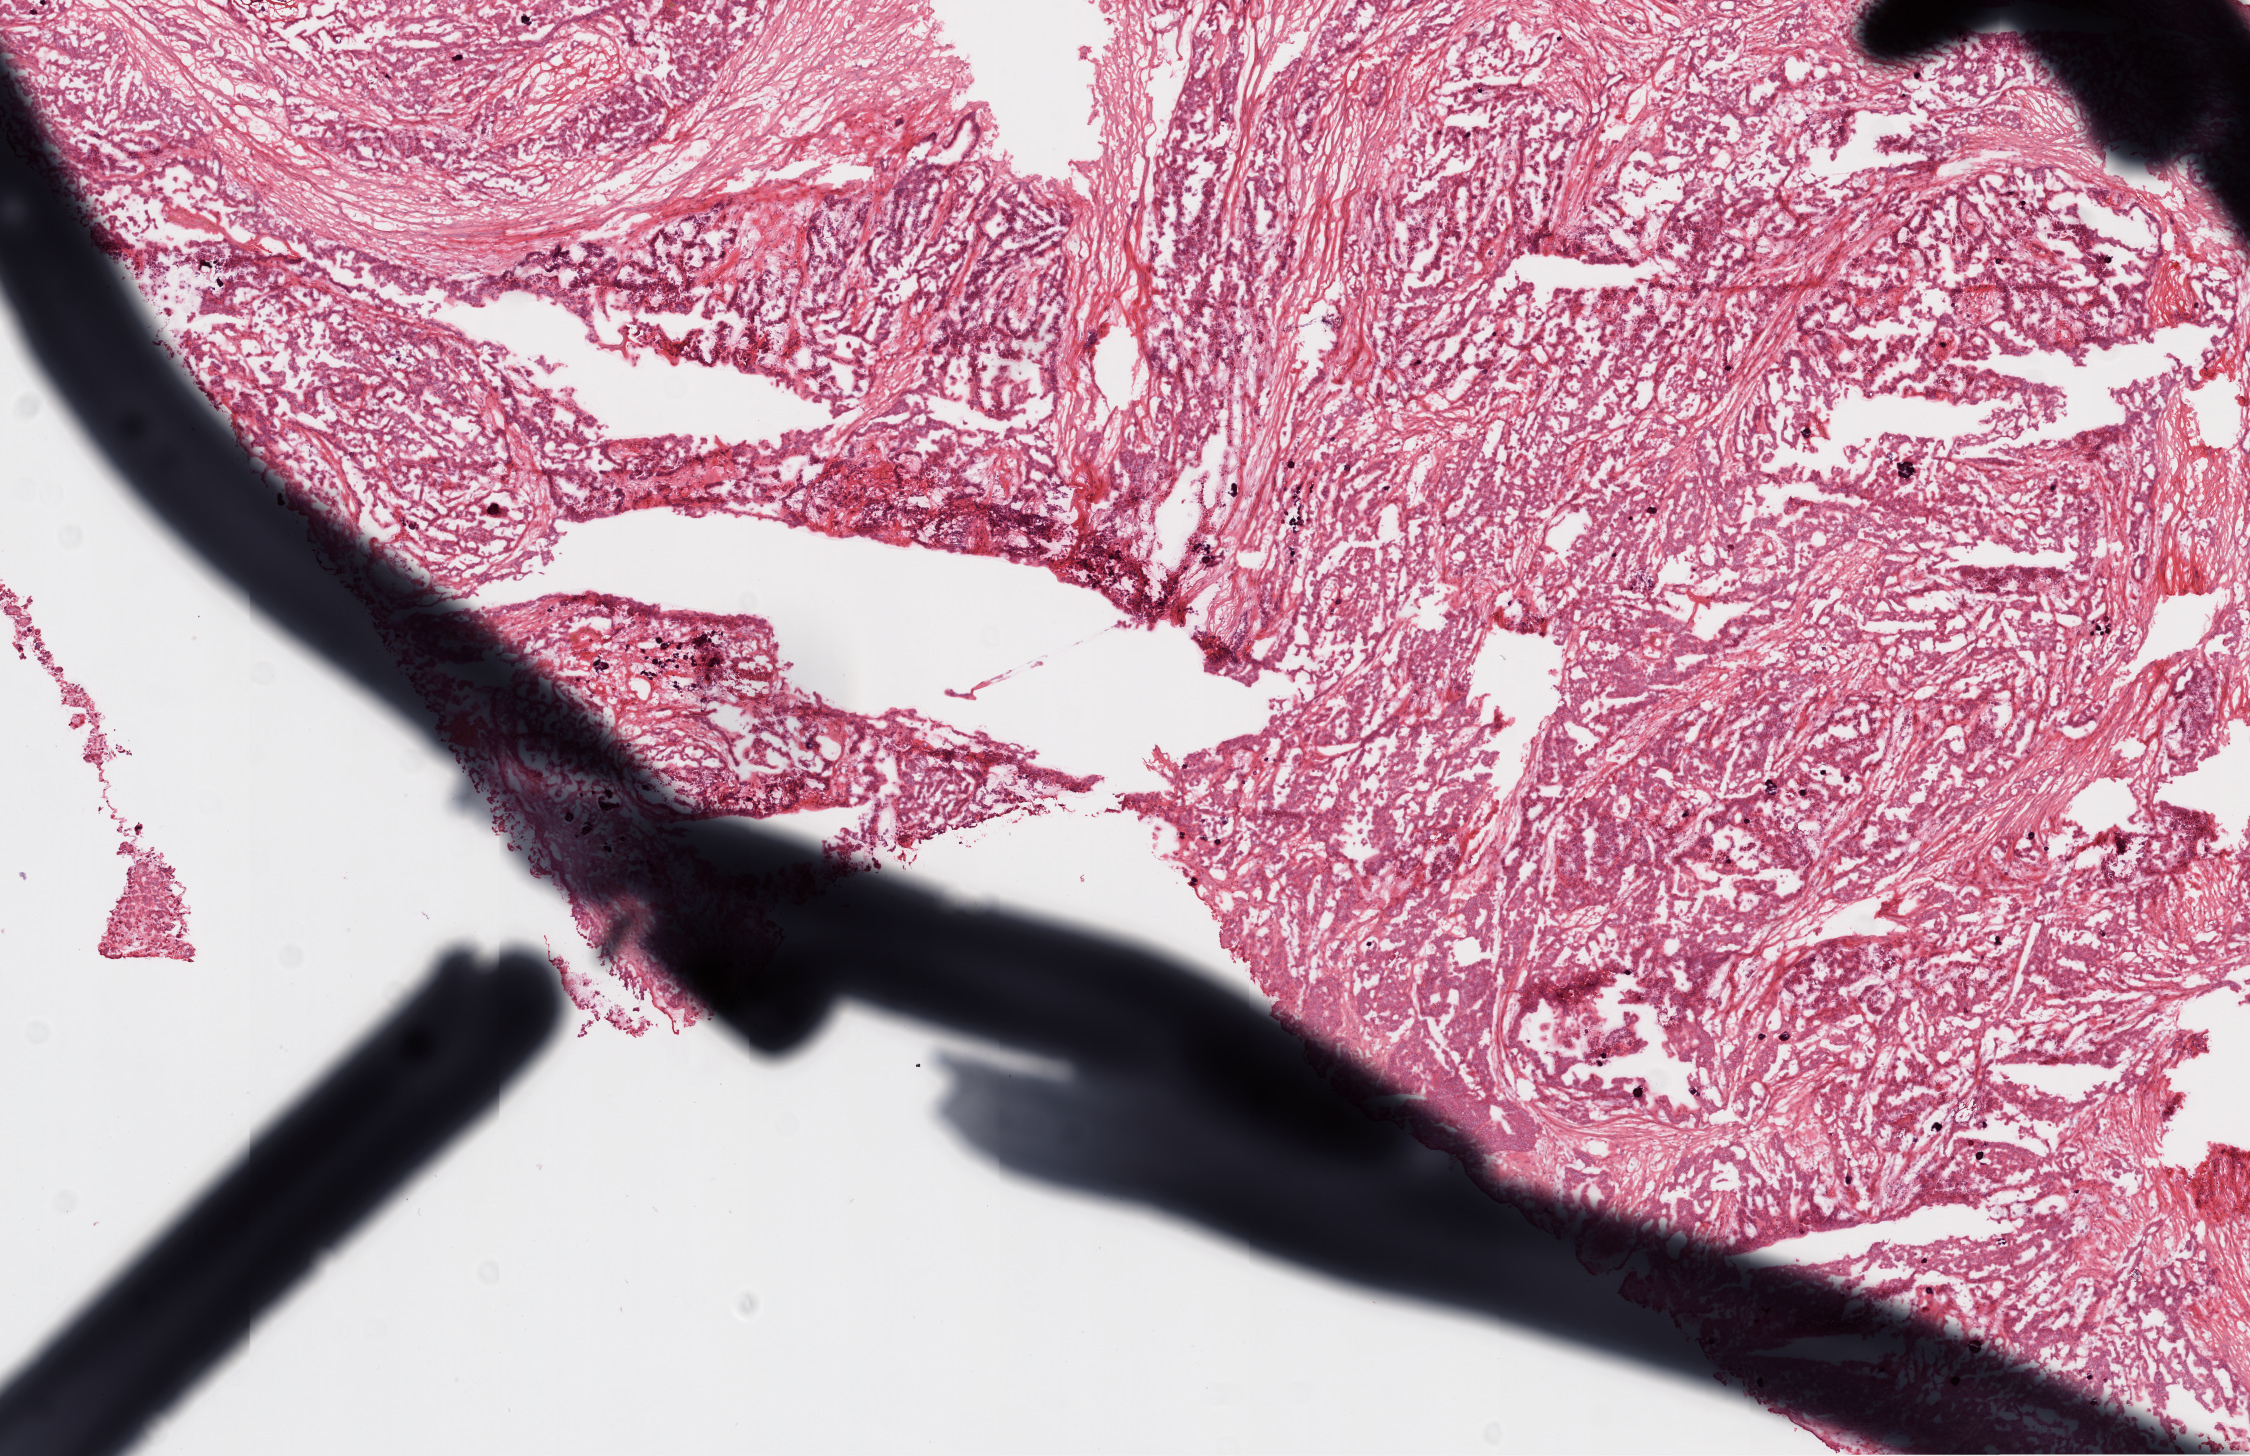
H&E whole-slide image, shown as a low-resolution overview of the whole scanned area (about 9.0 x 5.8 mm, acquisition: 20x scan), frozen section, sample: primary tumour, ovary. Female patient; age at initial diagnosis 55 years. Histologic grade: G2 (moderately differentiated). Pathologist review of this section (percent, as recorded): tumour cells 90%, tumour nuclei 90%, normal cells 0%, stromal cells 10%, necrosis 0%.
Laterality: bilateral. FIGO stage: IIIC. Pathologic diagnosis: Serous cystadenocarcinoma, NOS.